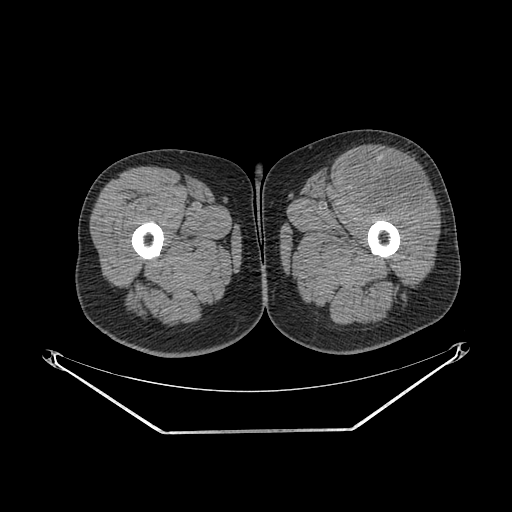
CT of an extremity soft-tissue mass (from a PET/CT study), one axial slice; position 242 of 267 along the scan axis; reconstruction kernel SOFT; 140 kVp; soft-tissue window (W 400 / L 40 HU); 3.75 mm slice thickness; 512 × 512 image matrix, field of view 500 × 500 mm. Male patient. Case-level facts recorded for this patient, not image findings: histological type: extraskeletal osteosarcoma; grade: high; site of the primary tumour: thigh.
Outlined on this slice (expert contour drawn on MRI and transferred to this co-registered scan by the dataset authors):
- gross tumour volume (mass): box from (x=352, y=160) to (x=428, y=211) px